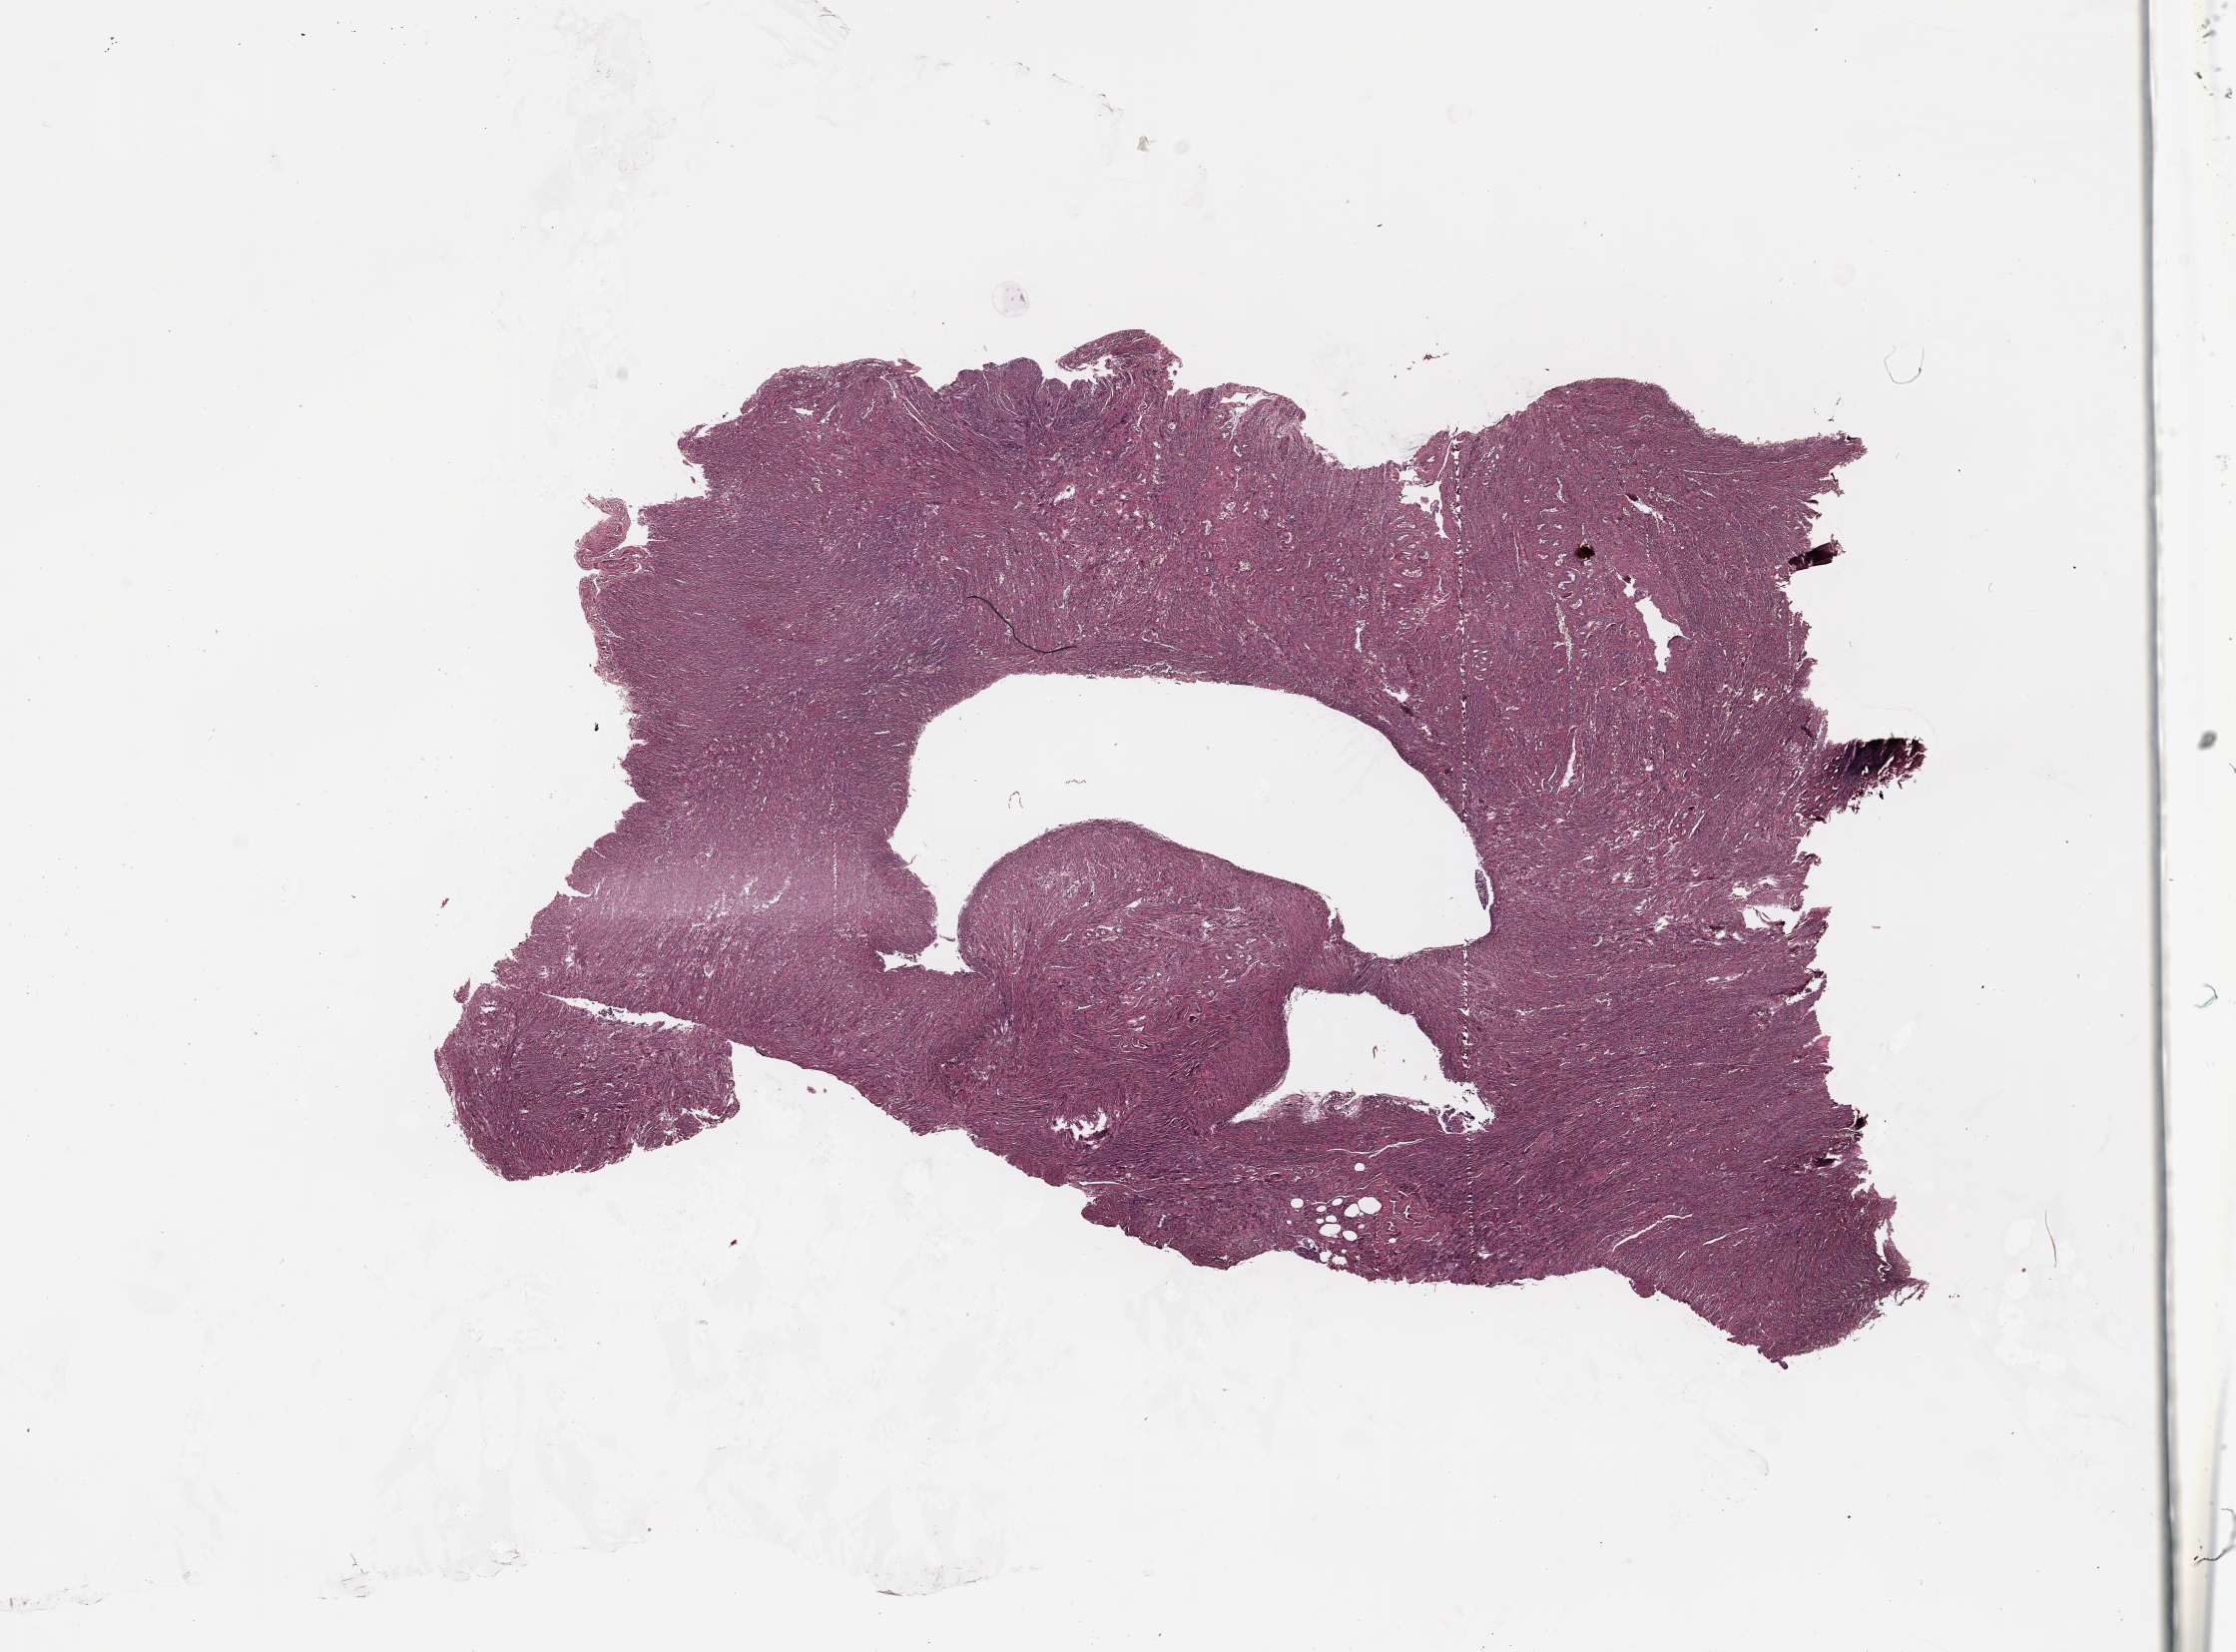
H&E-stained whole-slide image, low-resolution overview of the scanned area, about 17.7 x 13.1 mm. Uterus, normal (non-tumour) tissue. Female, 58 y/o.
* this section: normal (non-tumour) tissue from the same patient
* patient diagnosis: Endometrioid adenocarcinoma, NOS